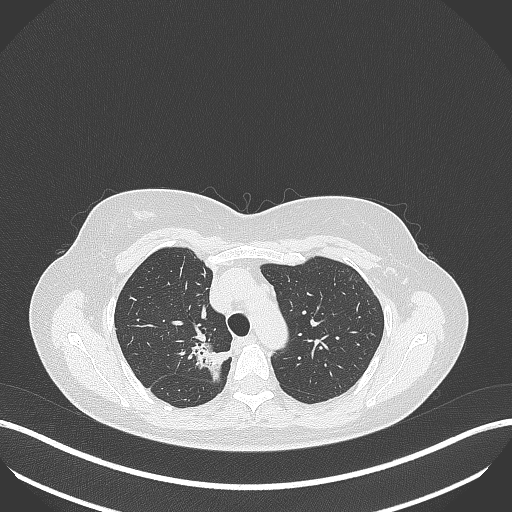
Chest CT, one axial slice; slice 294 of 386 in the series (ordered by position); reconstruction kernel B70f; 120 kVp; lung window (W 1500 / L -600 HU); 512 × 512 image matrix, field of view 400 × 400 mm. Female patient, age 65 years. Case-level facts recorded for this patient, not image findings: clinical TNM (as recorded): T1b N0 M0; histopathological grade: G2.
Structures marked on this image (bounding box drawn by a radiologist):
- lung tumour (recorded histology: adenocarcinoma): bounding box <189,337,233,386> (left, top, right, bottom; pixels)